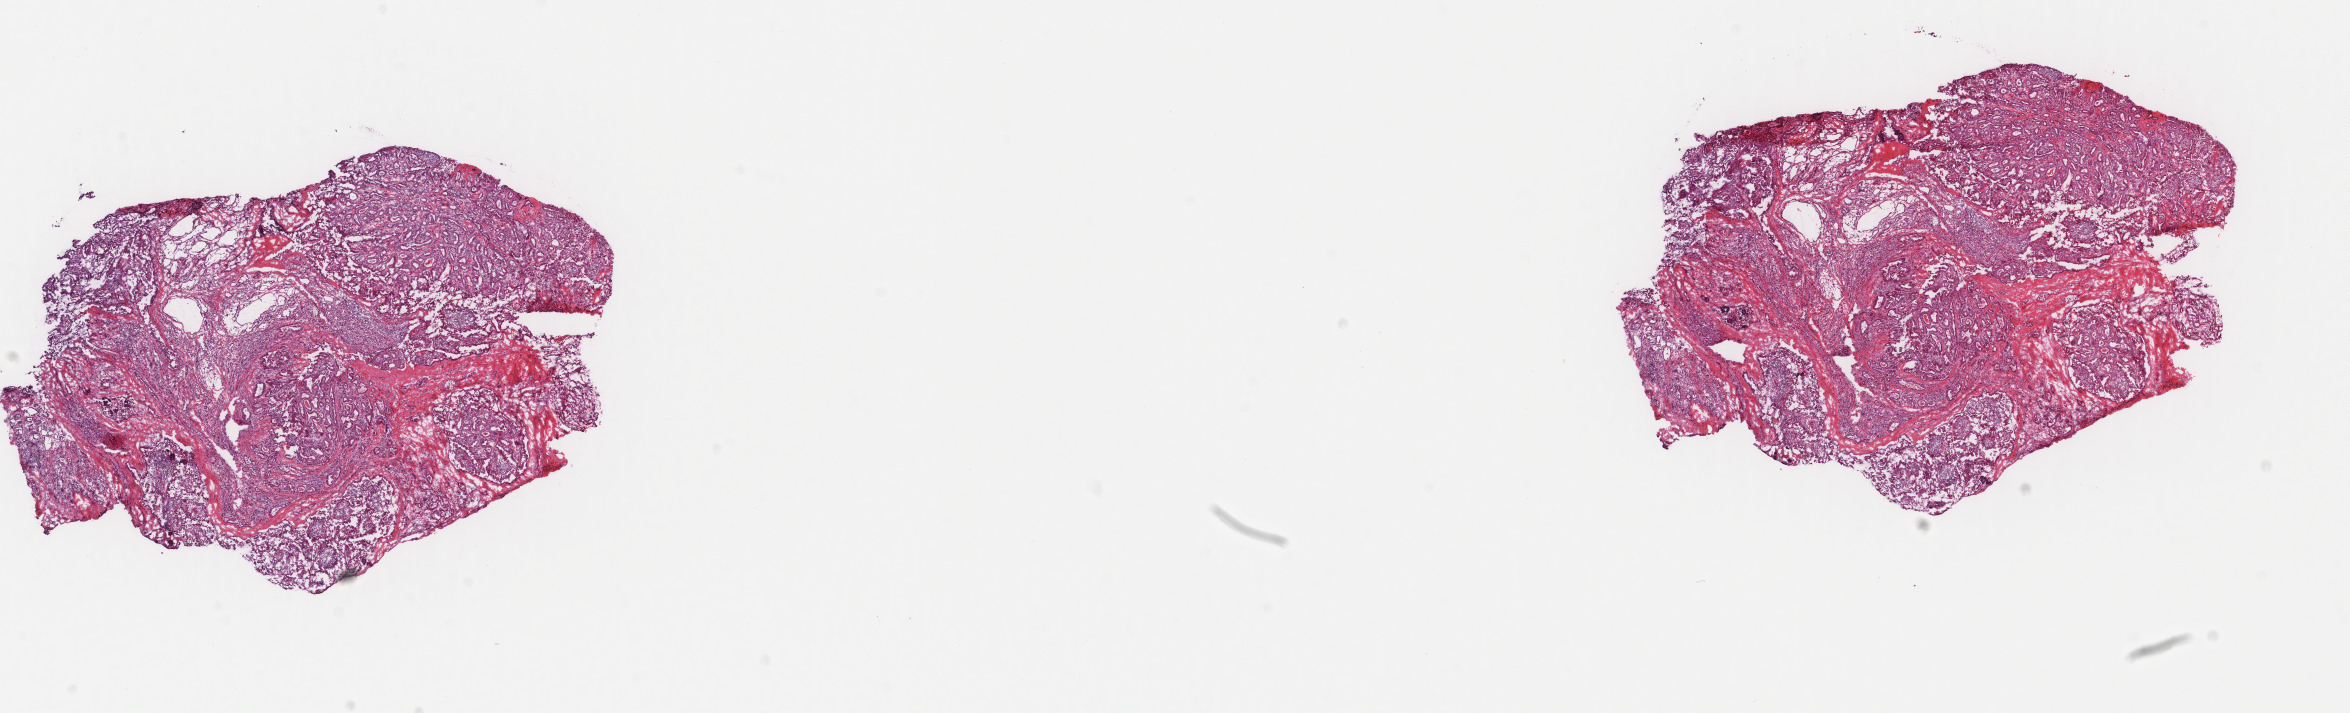
Hematoxylin and eosin (H&E) stained whole-slide image — whole scanned area (about 18.7 x 5.7 mm, from a 40x scan) shown as a low-resolution overview; frozen section; sample: primary tumour, thyroid. Patient: male, age at initial diagnosis 33 years. Composition of this section per pathologist review: tumour cells 80%, tumour nuclei 80%, normal cells 0%, stromal cells 20%, necrosis 0%. Inflammatory infiltration, as recorded: lymphocyte infiltration 5%, monocyte infiltration 0%, neutrophil infiltration 0%.
TNM: T2 N1b MX. Laterality: left. Histologic diagnosis: Papillary adenocarcinoma, NOS (thyroid gland). Lymph nodes positive (case pathology): 15 of 54 examined. AJCC pathologic stage: I (7th edition).